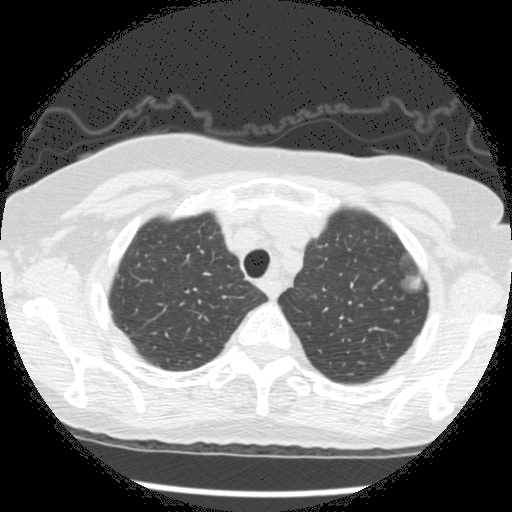
Low-dose screening chest CT, one axial slice; slice 232 of 266 in the series (ordered by position); lung window (W 1500 / L -600 HU); 2.5 mm slice thickness; 512 × 512 image matrix, field of view 320 × 320 mm.
Annotated regions visible in this slice (outlined manually by an expert reader):
- lesion 1 (tumor, upper lobe of left lung): bounding box [x1, y1, x2, y2] px = [408, 276, 421, 290]